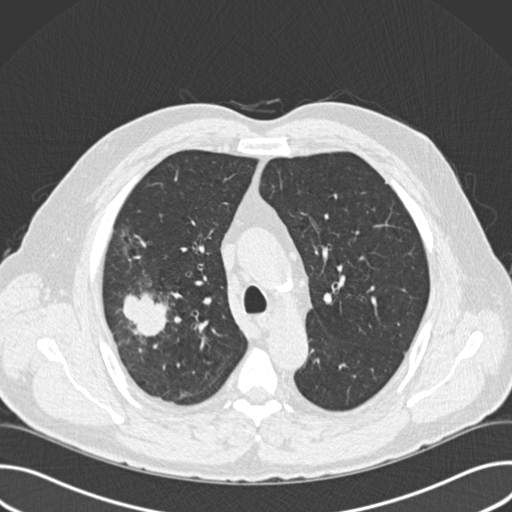
Low-dose screening chest CT, one axial slice; reconstruction kernel B30f; 120 kVp; lung window (W 1500 / L -600 HU); 512 × 512 image matrix, field of view 380 × 380 mm.
Annotated regions visible in this slice (expert manual segmentation):
- lesion 1 (tumor, upper lobe of right lung): bounding box <123,292,169,337> (left, top, right, bottom; pixels)